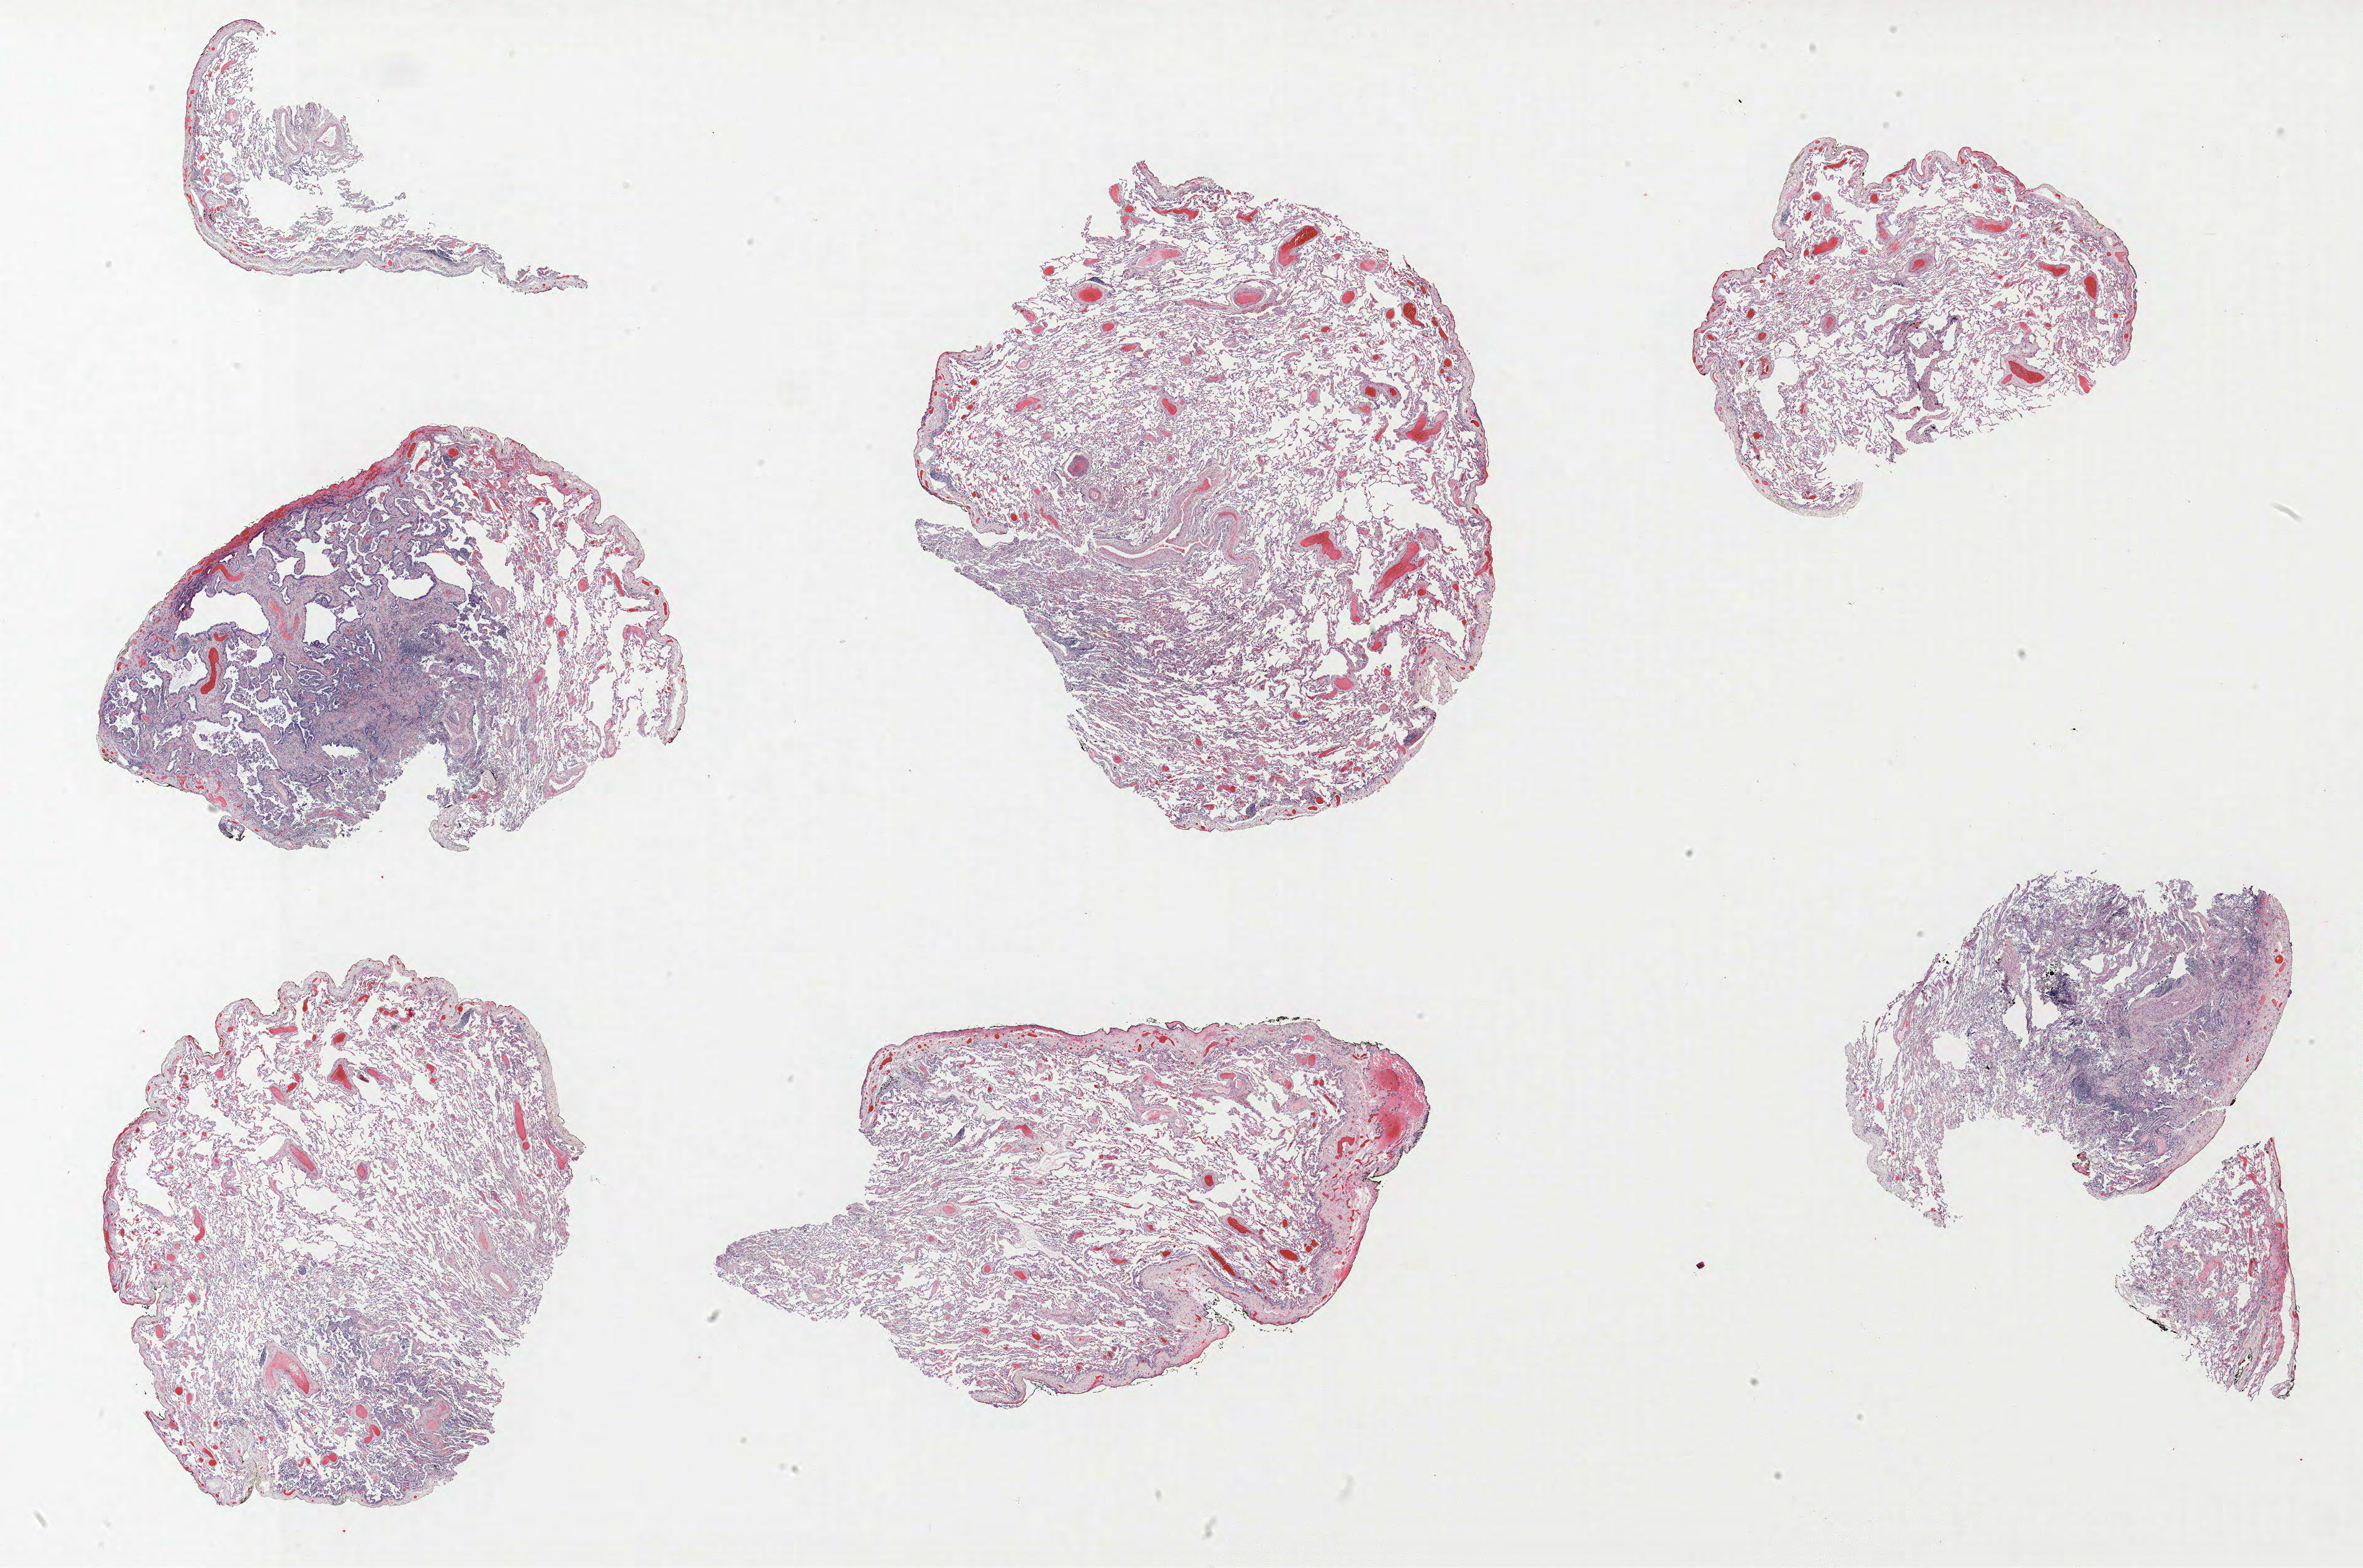
H&E-stained whole-slide image, low-resolution overview of the scanned area, about 30.5 x 20.2 mm; formalin-fixed paraffin-embedded (FFPE) section; lung. Male patient, aged 64 at enrolment. Former smoker at enrolment. Grade: poorly differentiated (G3).
Participant's lung-cancer diagnosis: Bronchiolo-alveolar adenocarcinoma, NOS. Primary tumour location (clinical record): right upper lobe. Tumour size (pathology): 5 mm. Stage (AJCC 6th edition): IA. Note: participant had 2 primary lung cancers recorded; fields above describe the first.